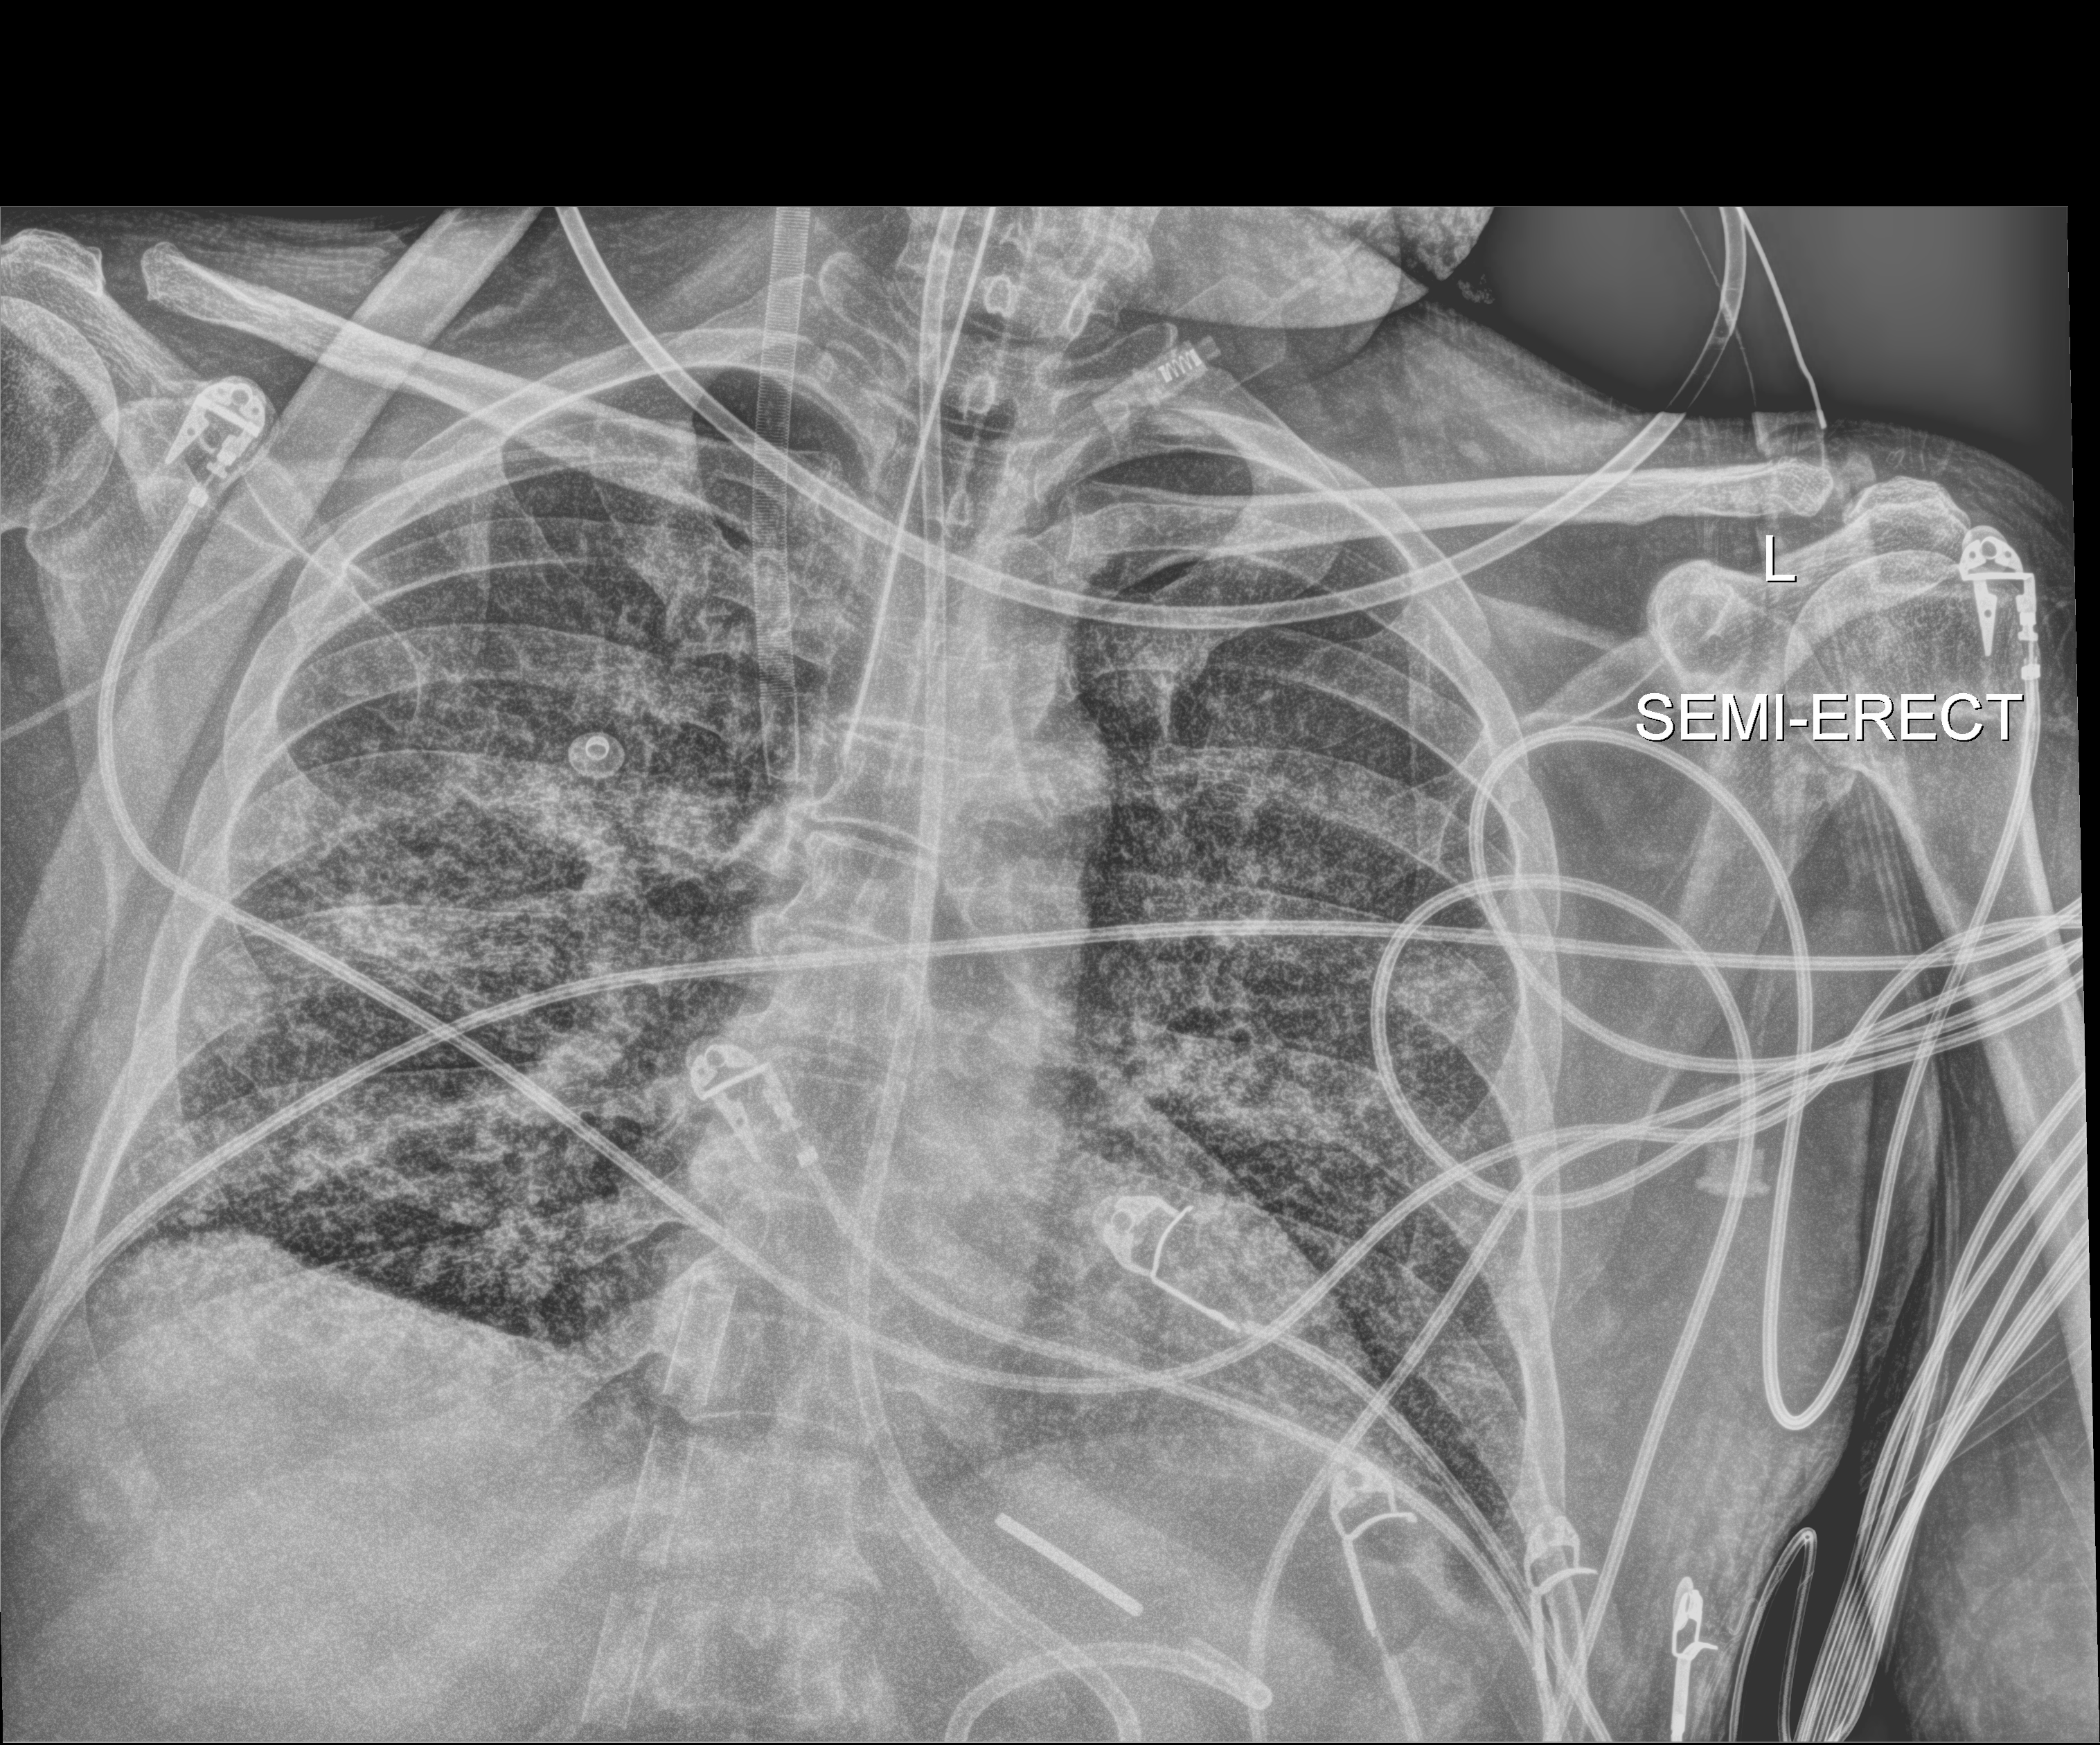
Portable chest radiograph; anteroposterior (AP) projection. Male patient hospitalised with COVID-19, age 18–59 years.
From the hospital-stay record, not from the radiograph (when in the stay this image was taken is not recorded): admitted to intensive care during this hospital stay: yes.